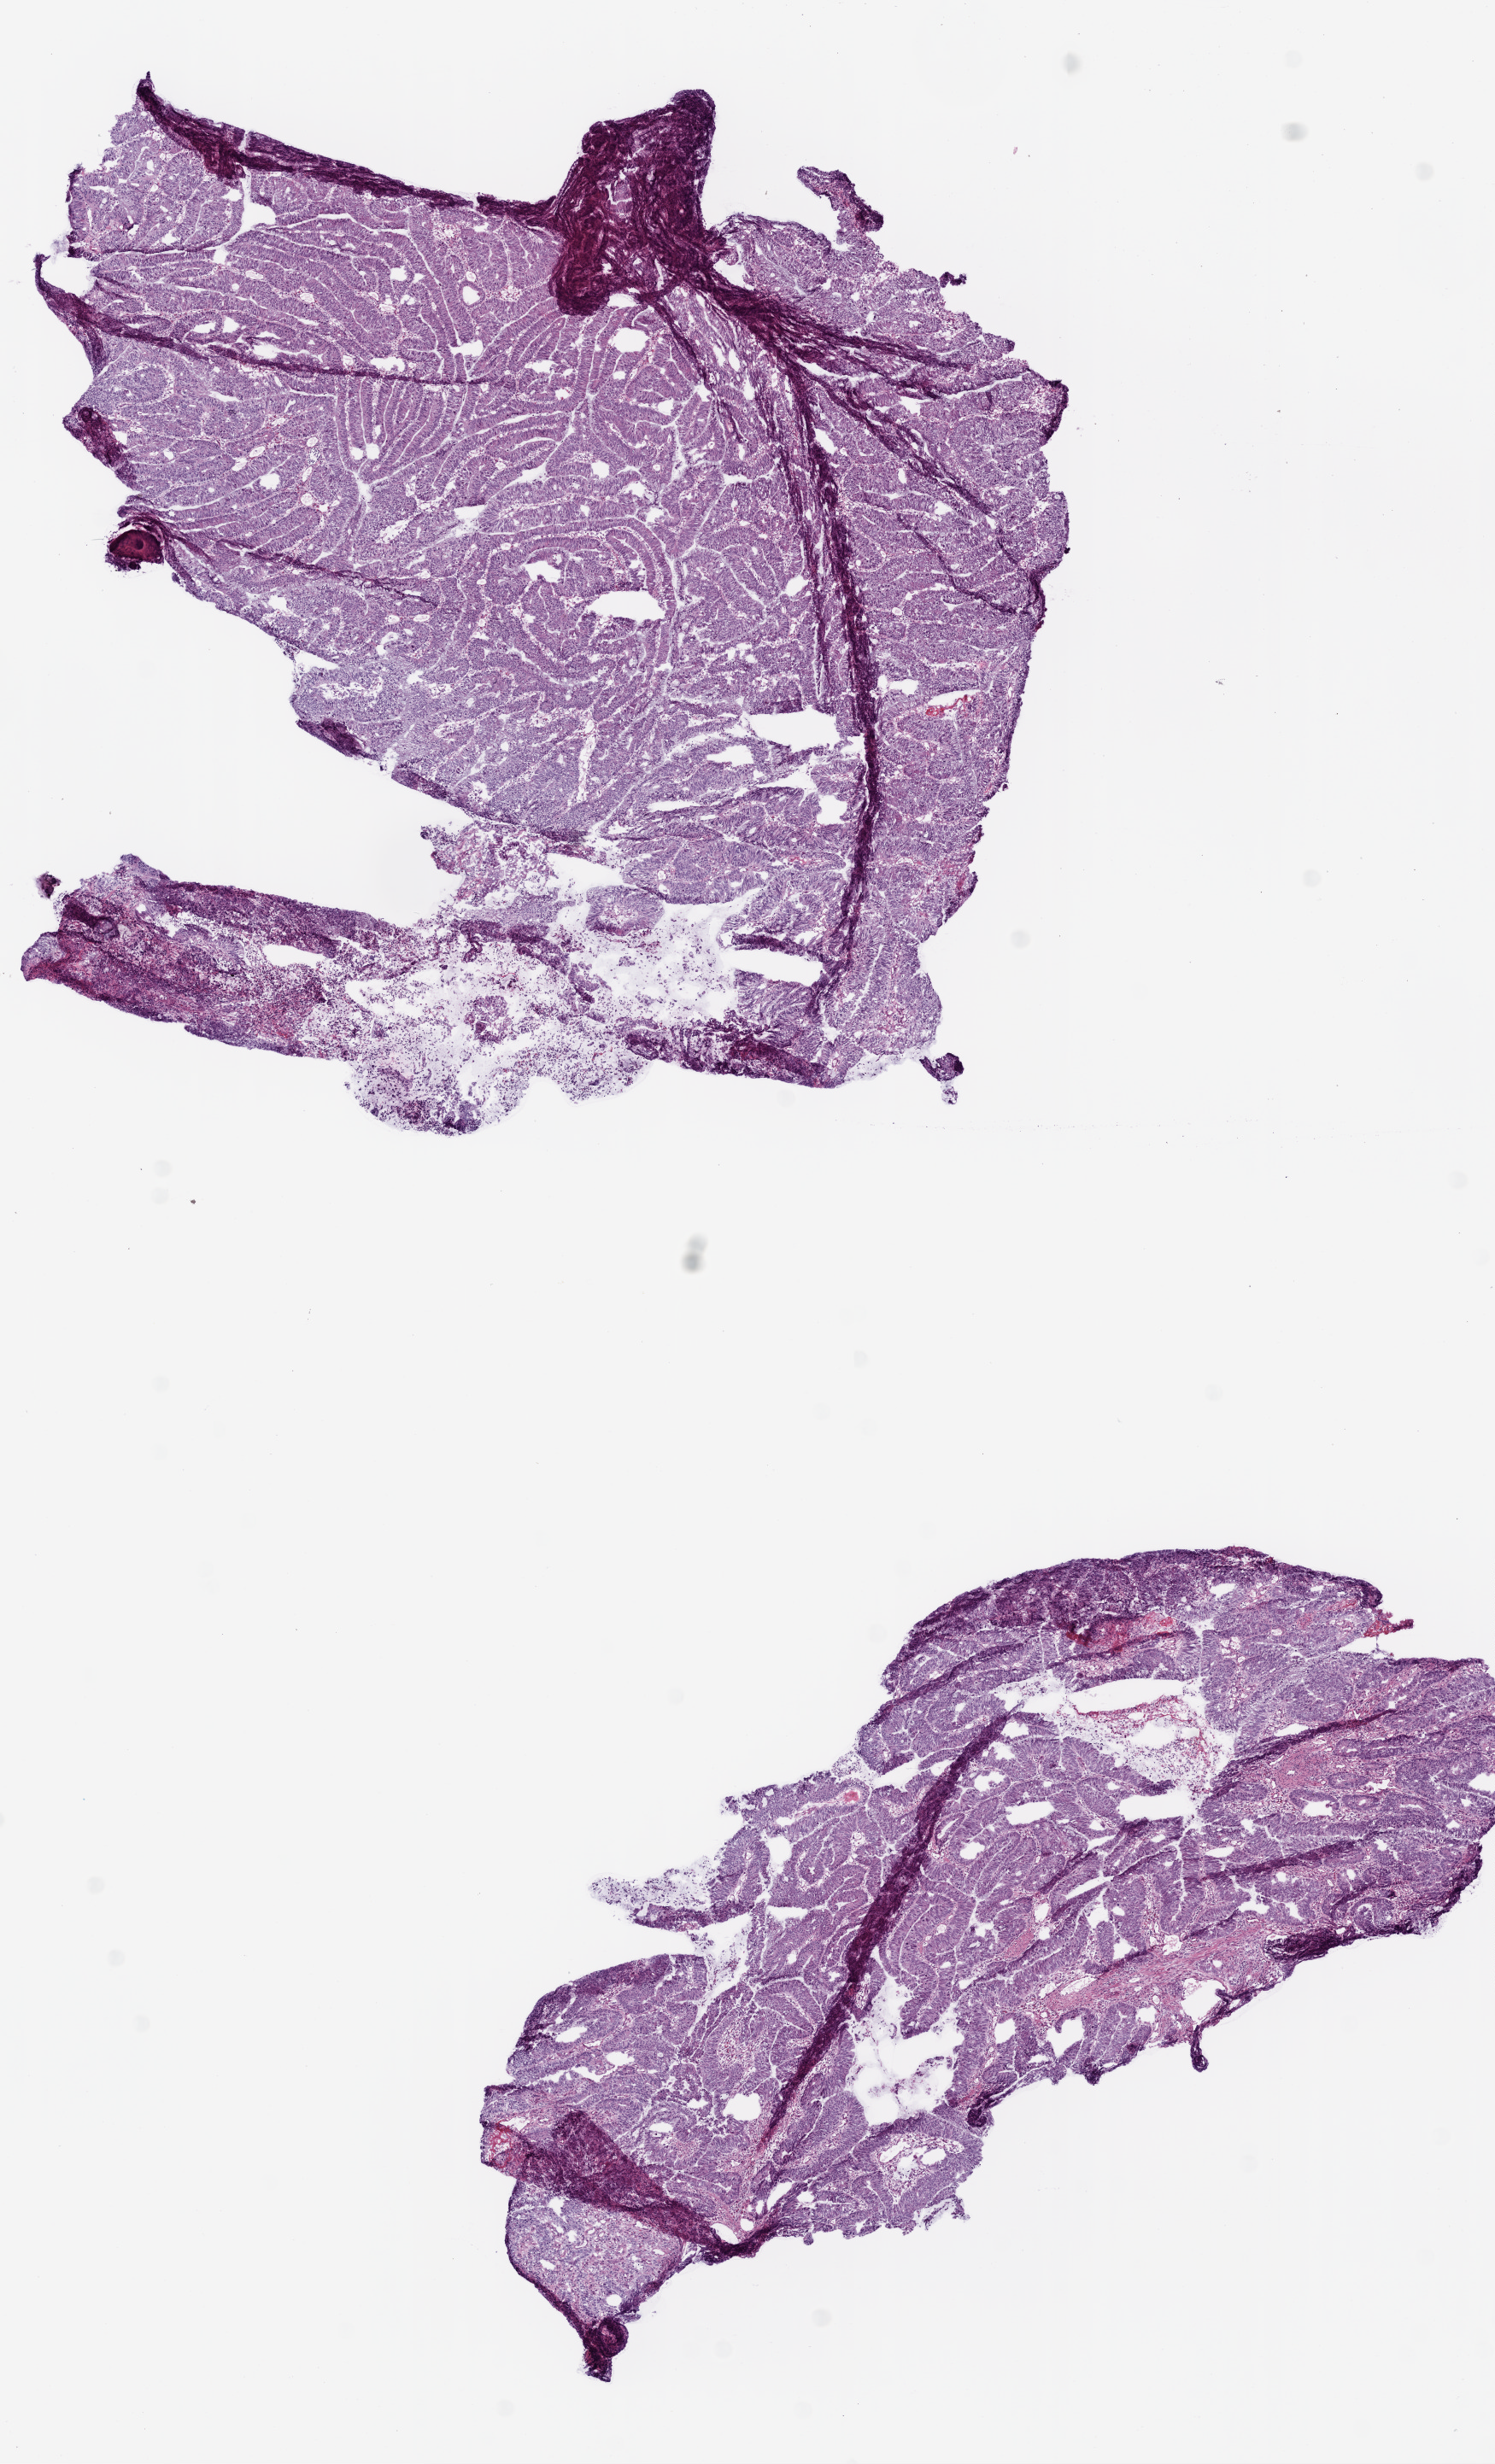
Whole-slide histology image, Hematoxylin and eosin (H&E) stained, low-resolution overview of the scanned area, about 7.0 x 11.6 mm. Frozen section from the top of the tissue portion. Sample: primary tumour, rectum. Female patient; age at initial diagnosis 76 years. Composition of this section per pathologist review: tumour cells 92%, tumour nuclei 90%, normal cells 0%, stromal cells 3%, necrosis 5%.
Pathologic diagnosis: Mucinous adenocarcinoma (rectosigmoid junction). AJCC pathologic stage: IIA (6th edition). Lymph nodes positive (case pathology): 0 of 25 examined. TNM: T3 N0 M0.